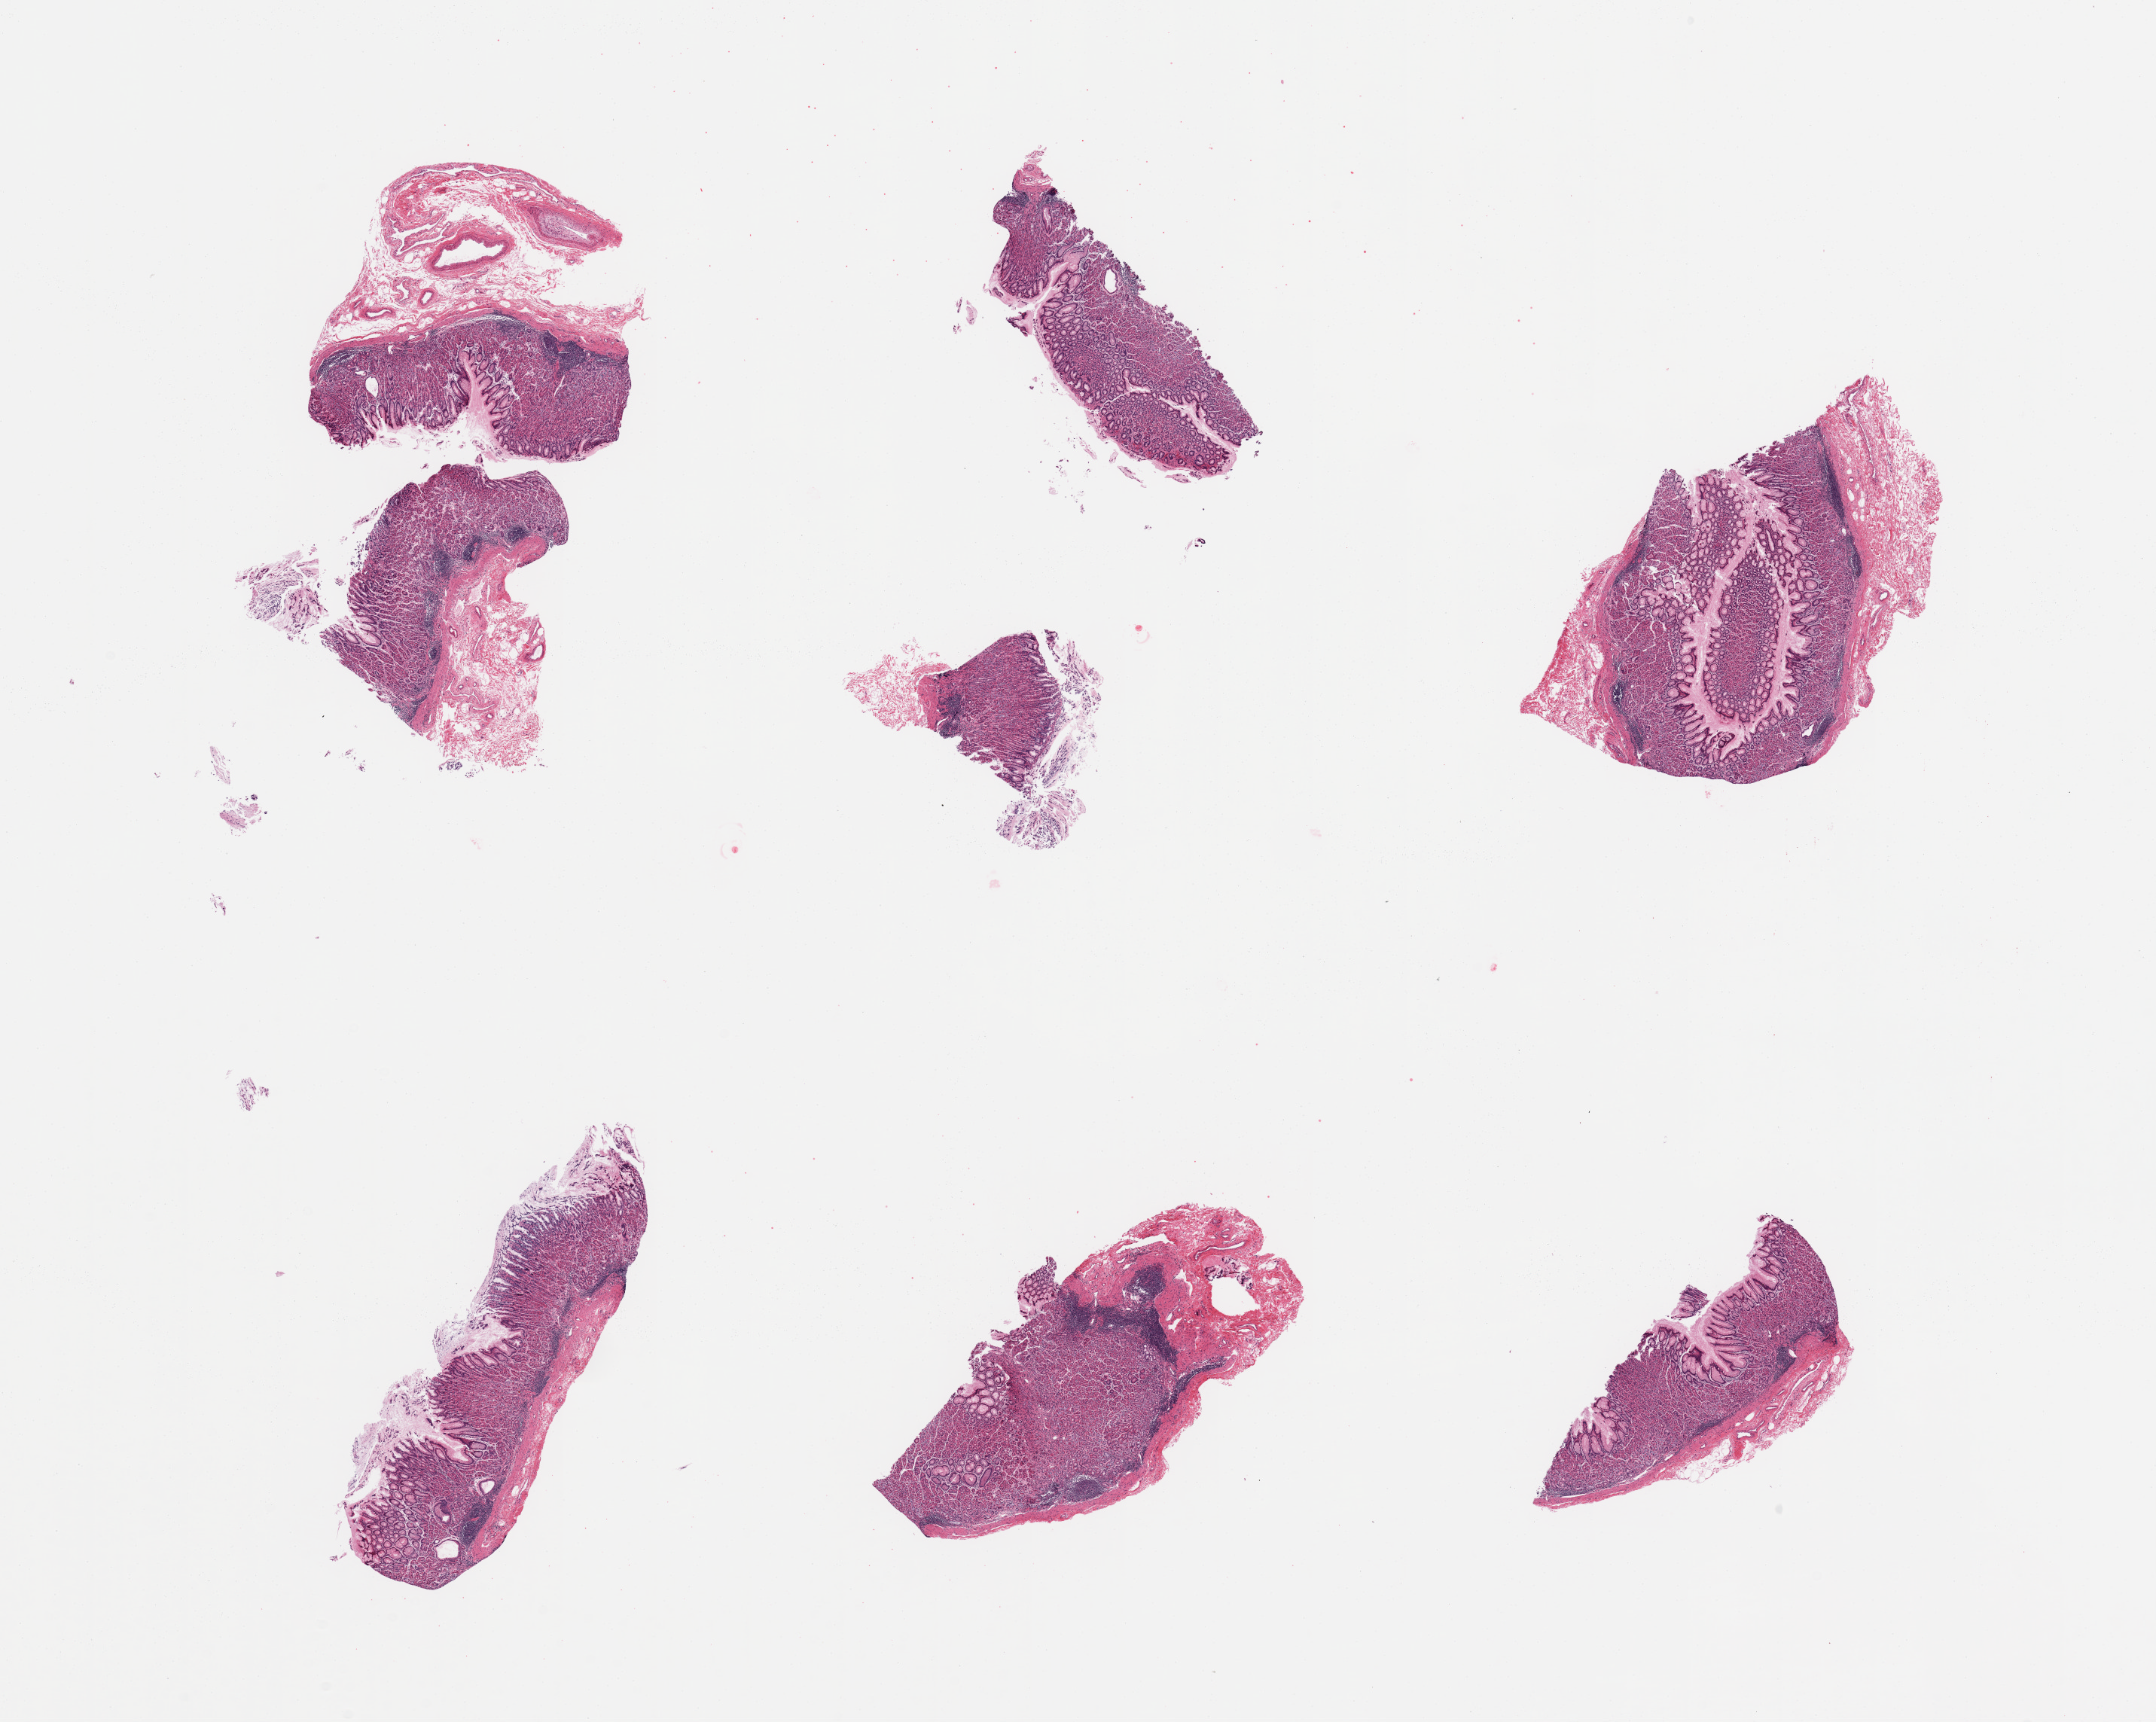
Digitized hematoxylin and eosin (H&E)-stained section, brightfield, low-resolution overview of the scanned area, about 22.6 x 18.1 mm. PAXgene-fixed, paraffin-embedded tissue. Target tissue: stomach. Donor tissue sample. Donor sex: female.
Pathologist's review note for this sample: 6 pieces, ~80% mucosa, chronic gastritis; lymphoid aggregates.